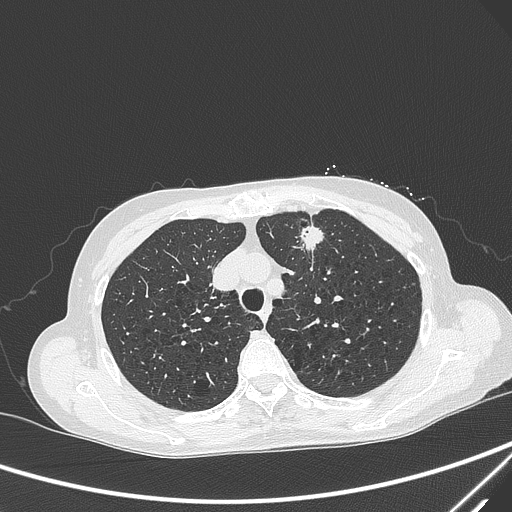
Chest CT, one axial slice. Lung window (W 1500 / L -600 HU). 512 × 512 image matrix. Patient: female, 71 years. Case-level facts recorded for this patient, not image findings: clinical TNM (as recorded): T1c N0 M0; histopathological grade: G2-3.
Outlined on this slice (bounding box drawn by a radiologist):
- lung tumour (recorded histology: adenocarcinoma): bounding box [x1, y1, x2, y2] px = [296, 215, 331, 267]